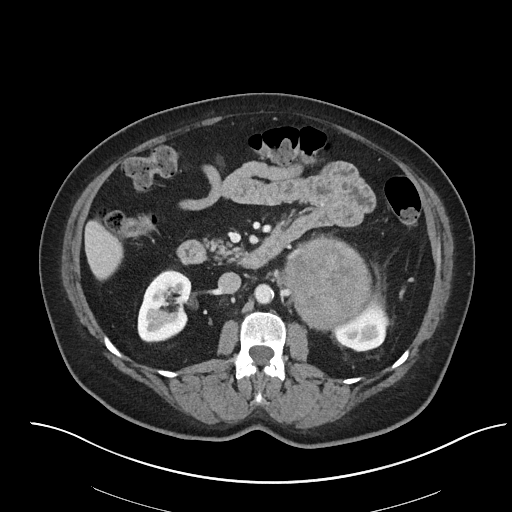
Contrast-enhanced abdominal CT, one axial slice; slice 33 of 92 in the series (ordered by position); 120 kVp; intravenous contrast given; soft-tissue window (W 400 / L 40 HU); 3 mm slice thickness; 512 × 512 image matrix. Patient: female, 53 years. From the clinical record (not read from this slice): diagnosis: adrenocortical carcinoma; tumour side: left adrenal; tumour size at pathology: 9 cm; Ki-67 index: 28 %; stage (as recorded): 2.
Annotated regions visible in this slice (semi-automatic segmentation, software-assisted and operator-edited):
- mass: bounding box (x1, y1, x2, y2) in pixels: (284, 242, 371, 326)